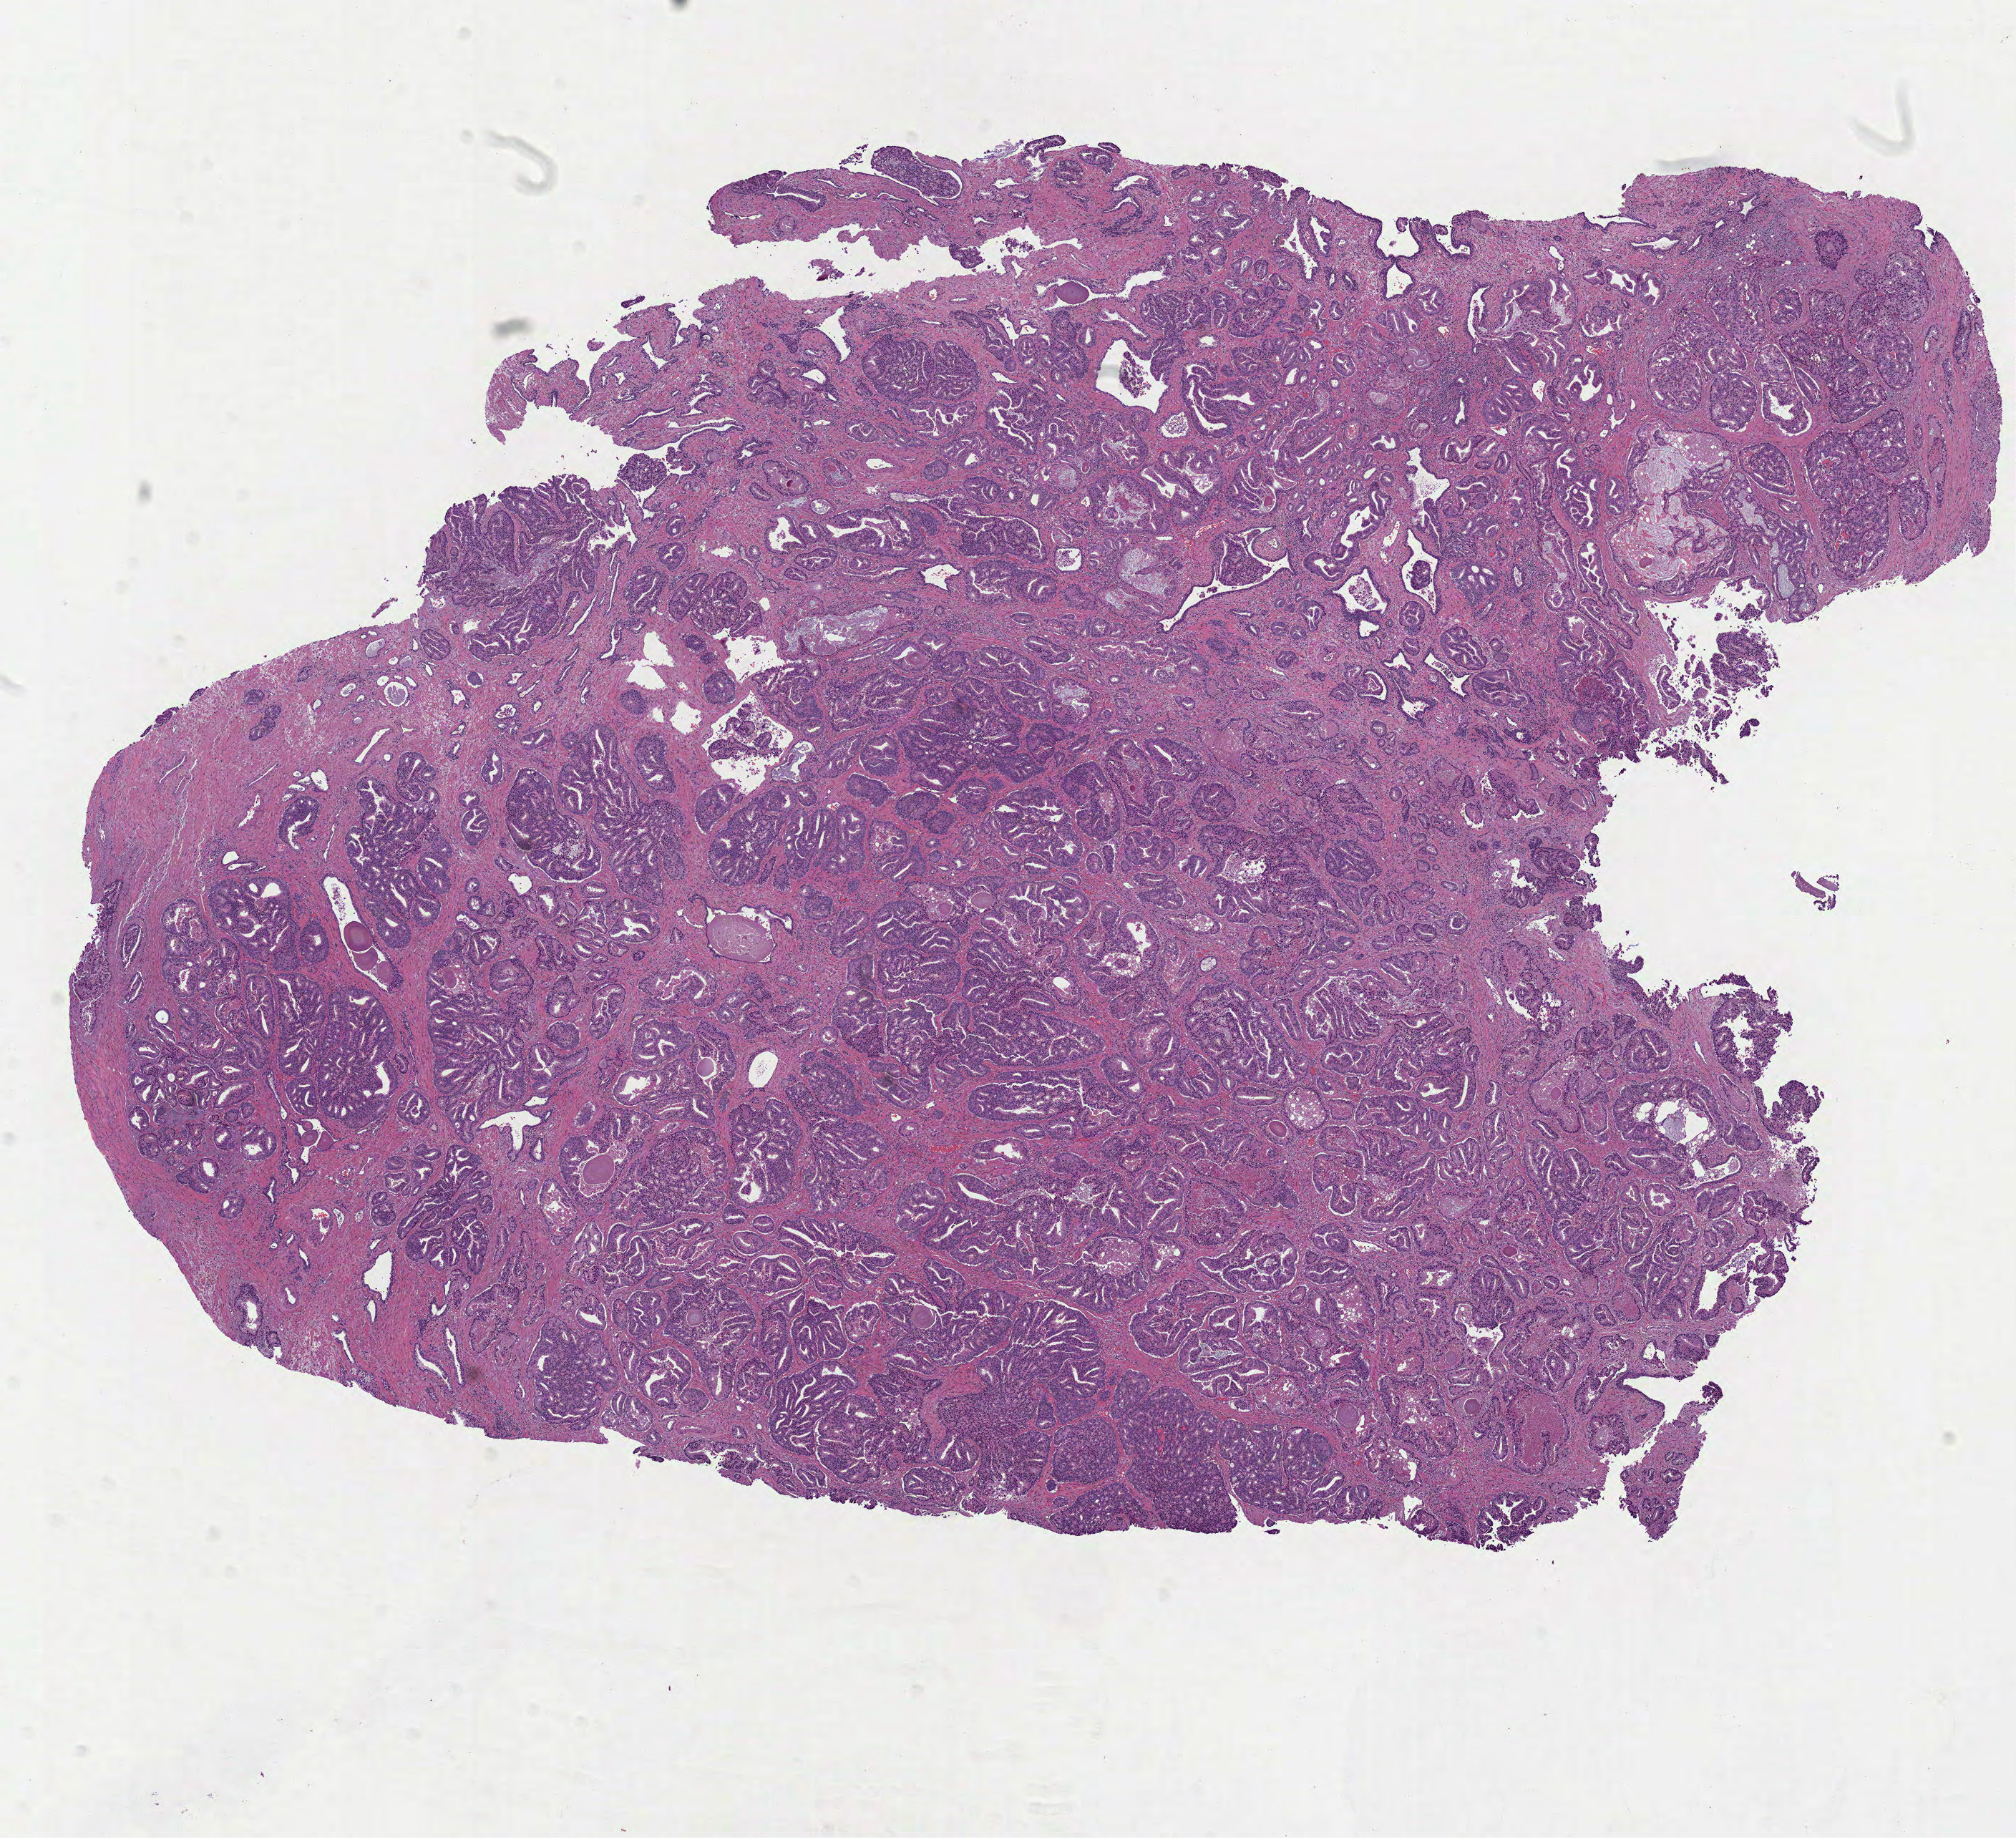
Digitized H&E tissue section (whole slide) — shown as a low-resolution overview of the whole scanned area (about 11.4 x 10.4 mm, from a 40x scan); formalin-fixed paraffin-embedded (FFPE) diagnostic section; primary tumour sample from the prostate. Male, age 46 years at initial diagnosis.
Histologic diagnosis: Acinar cell carcinoma (prostate gland).